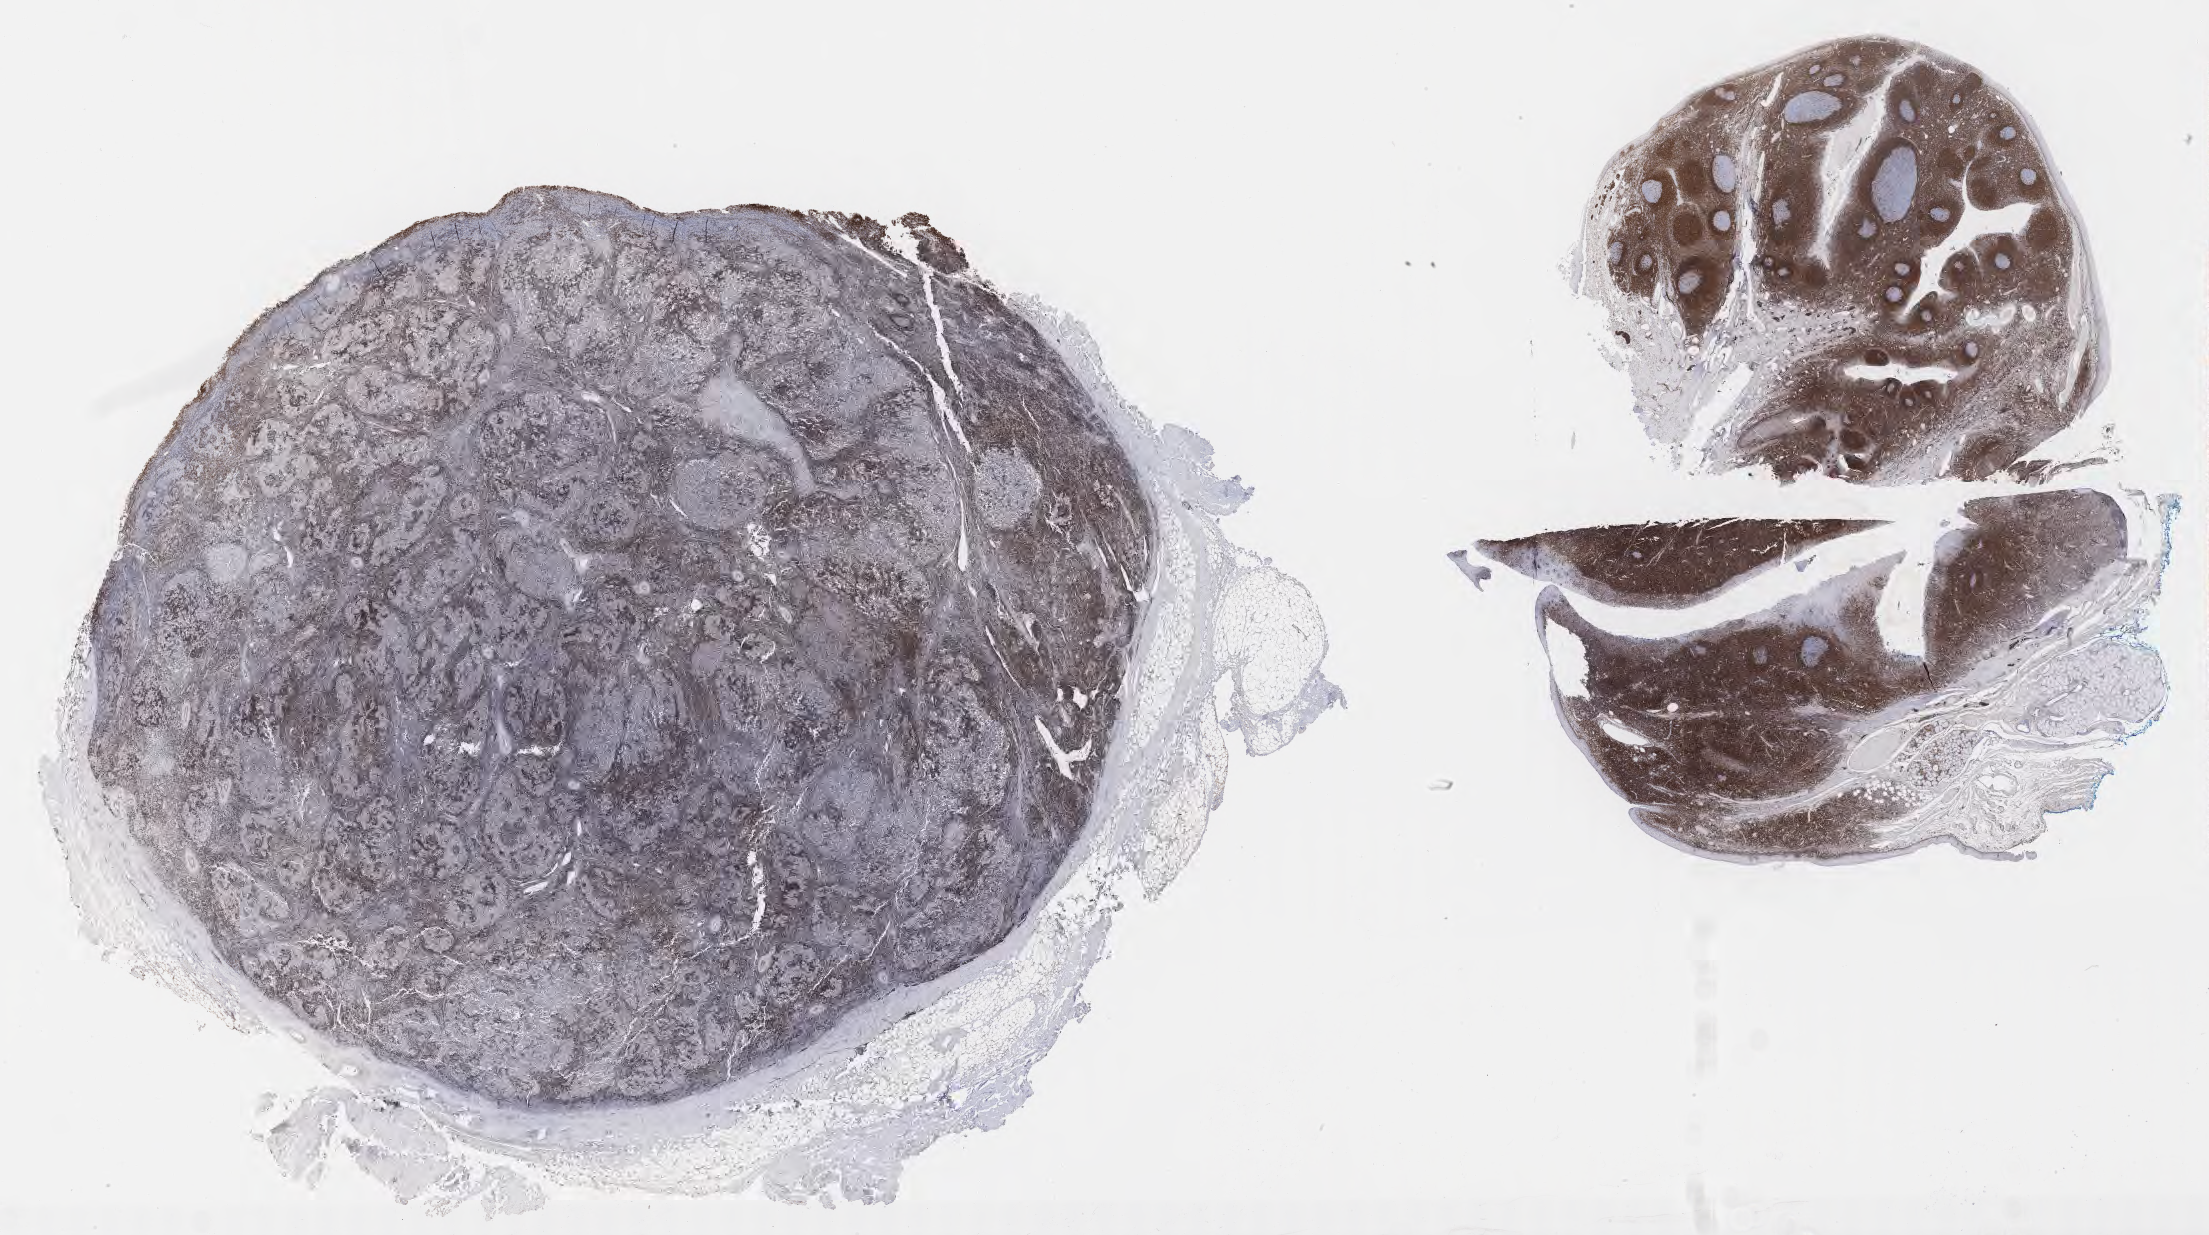
Immunohistochemistry (IHC) whole-slide image stained for BCL2, a low-resolution overview of the entire scanned area, about 35.7 x 20.0 mm. Tumor tissue. Anatomic site: lymph node. Male patient, 46 years old.
Histologic diagnosis: Diffuse large B-cell lymphoma, NOS.